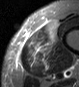
MRI of an extremity soft-tissue mass, one axial slice; position 9 of 45 along the scan axis; STIR; MR volume resampled by the dataset authors to the PET/CT grid (not the native acquisition matrix); 3.27 mm slice thickness; 79 × 87 image matrix. Male patient. Case-level facts recorded for this patient, not image findings: histological type: pleiomorphic leiomyosarcoma; grade: high; site of the primary tumour: left thigh.
Outlined on this slice (expert contour drawn on MRI and transferred to this co-registered scan by the dataset authors):
- gross tumour volume including surrounding oedema: bounding box [x1, y1, x2, y2] px = [25, 20, 58, 72]